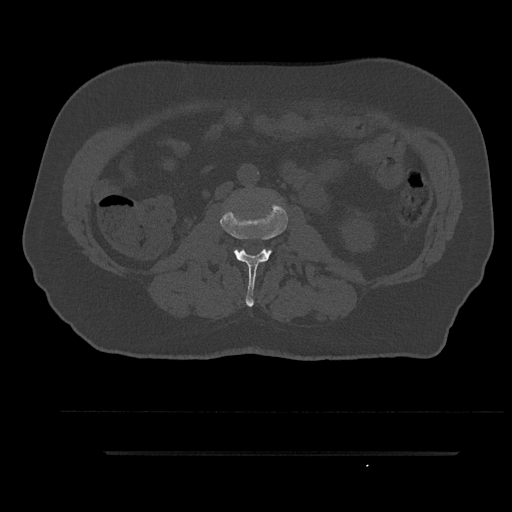
CT including the spine, one axial slice. Position 92 of 797 along the scan axis. Bone window (W 1800 / L 400 HU). 0.5 mm slice thickness. 512 × 512 image matrix. Patient: male, 63 years. Case-level facts recorded for this patient, not image findings: primary cancer: renal.
Annotated regions visible in this slice (semi-automatic segmentation, software-assisted and operator-edited):
- L2 vertebra: bounding box (x1, y1, x2, y2) in pixels: (220, 204, 288, 307)